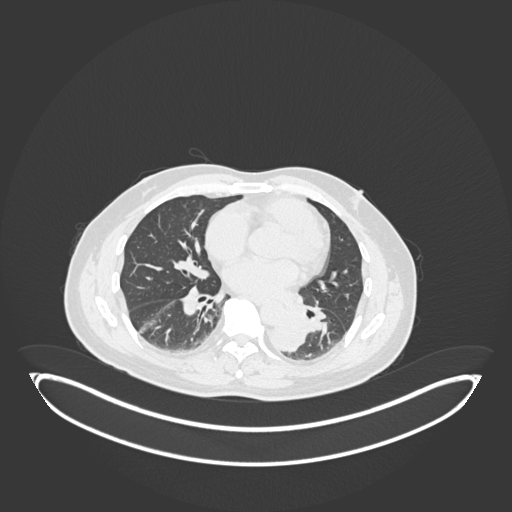
Chest CT, one axial slice. Slice 84 of 258 in the series (ordered by position). Reconstruction kernel B30f. Lung window (W 1500 / L -600 HU). 1 mm slice thickness. 512 × 512 image matrix, field of view 500 × 500 mm. Male patient, age 54 years. Case-level facts recorded for this patient, not image findings: clinical TNM (as recorded): T3 N0 M0.
Annotated regions visible in this slice (bounding box drawn by a radiologist):
- lung tumour (recorded histology: squamous cell carcinoma): bounding box (x1, y1, x2, y2) in pixels: (265, 305, 312, 353)